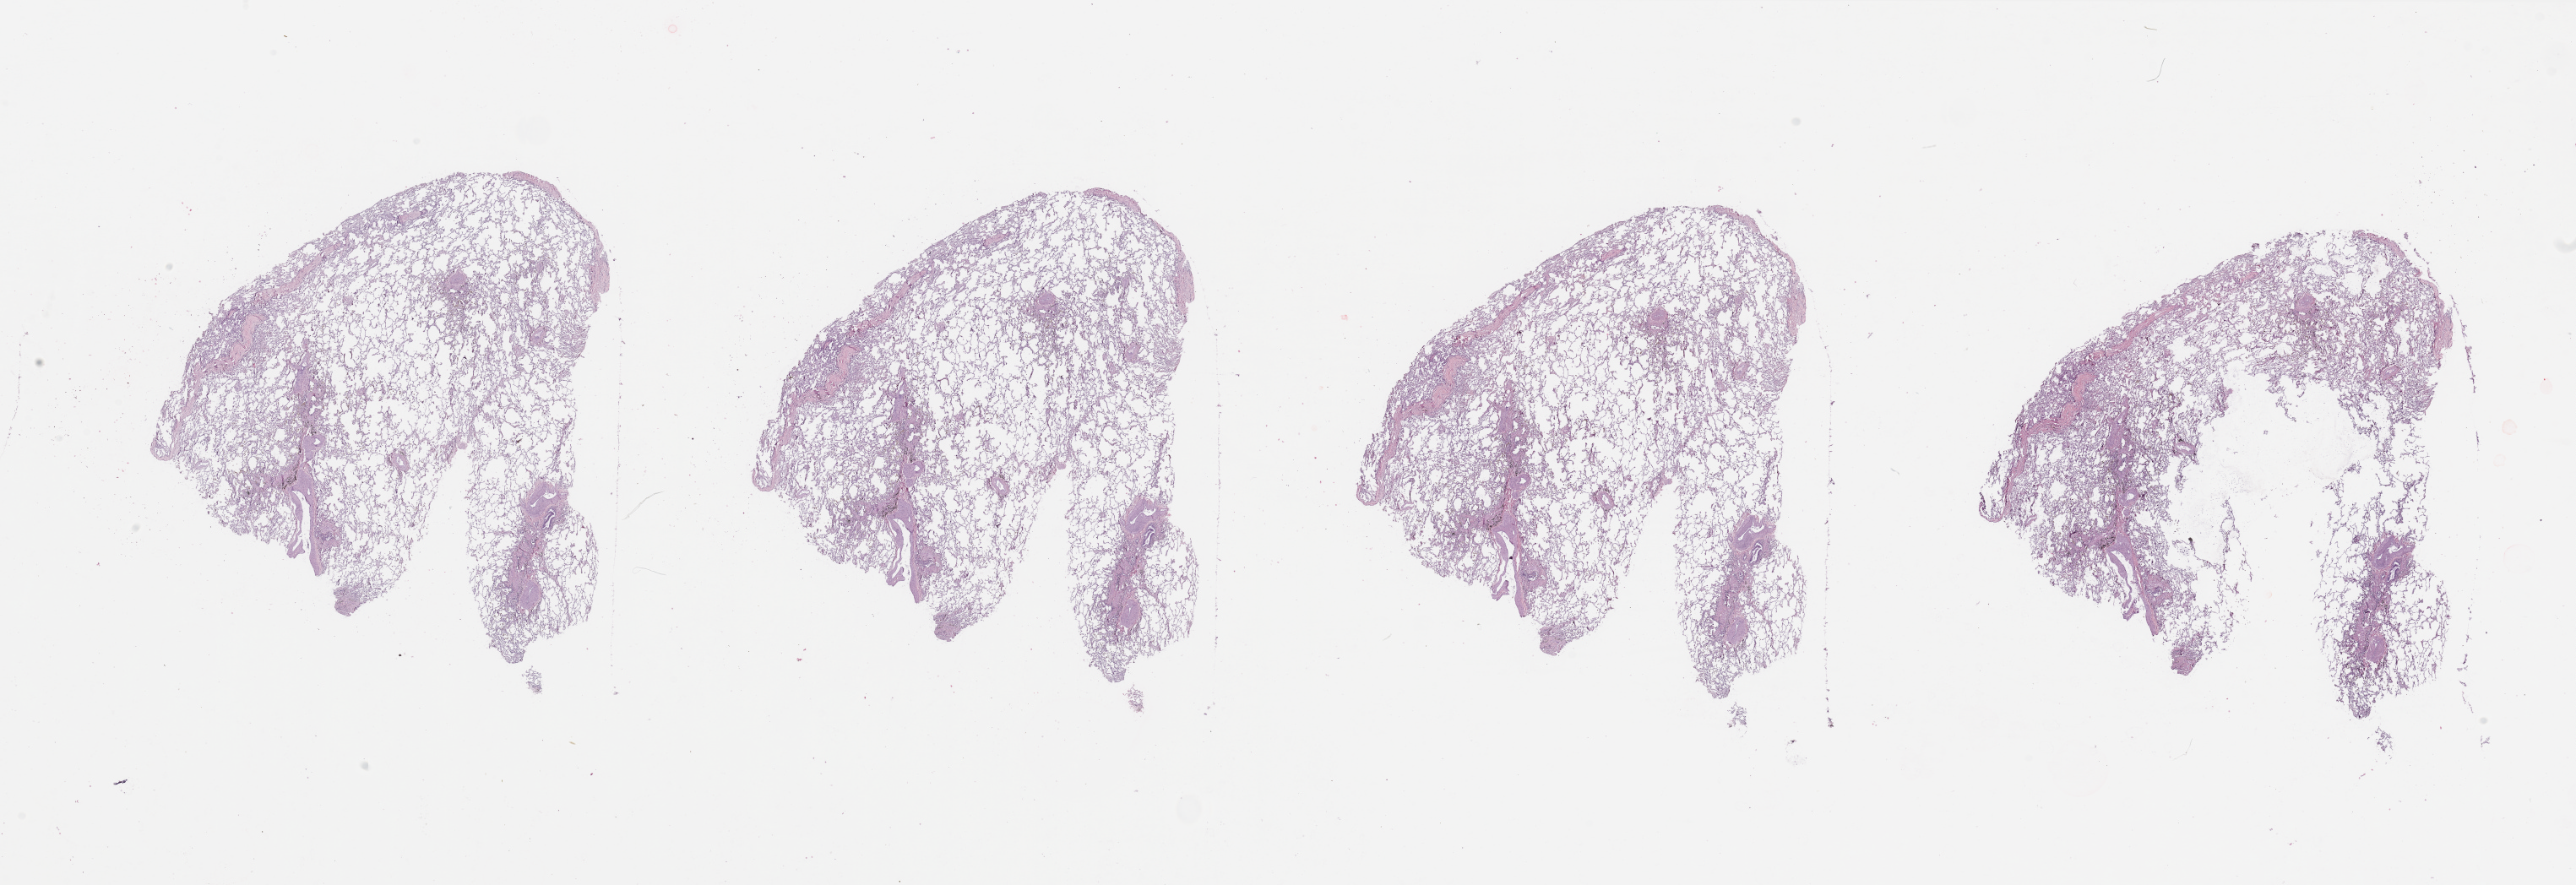
Whole-slide histology image, Hematoxylin and eosin (H&E) stained — low-resolution overview of the scanned area, about 48.2 x 16.6 mm. Normal (non-tumour) tissue sample, lung. Patient: male, age 51 years.
This section: normal (non-tumour) tissue from the same patient. Patient diagnosis: Adenocarcinoma, NOS.